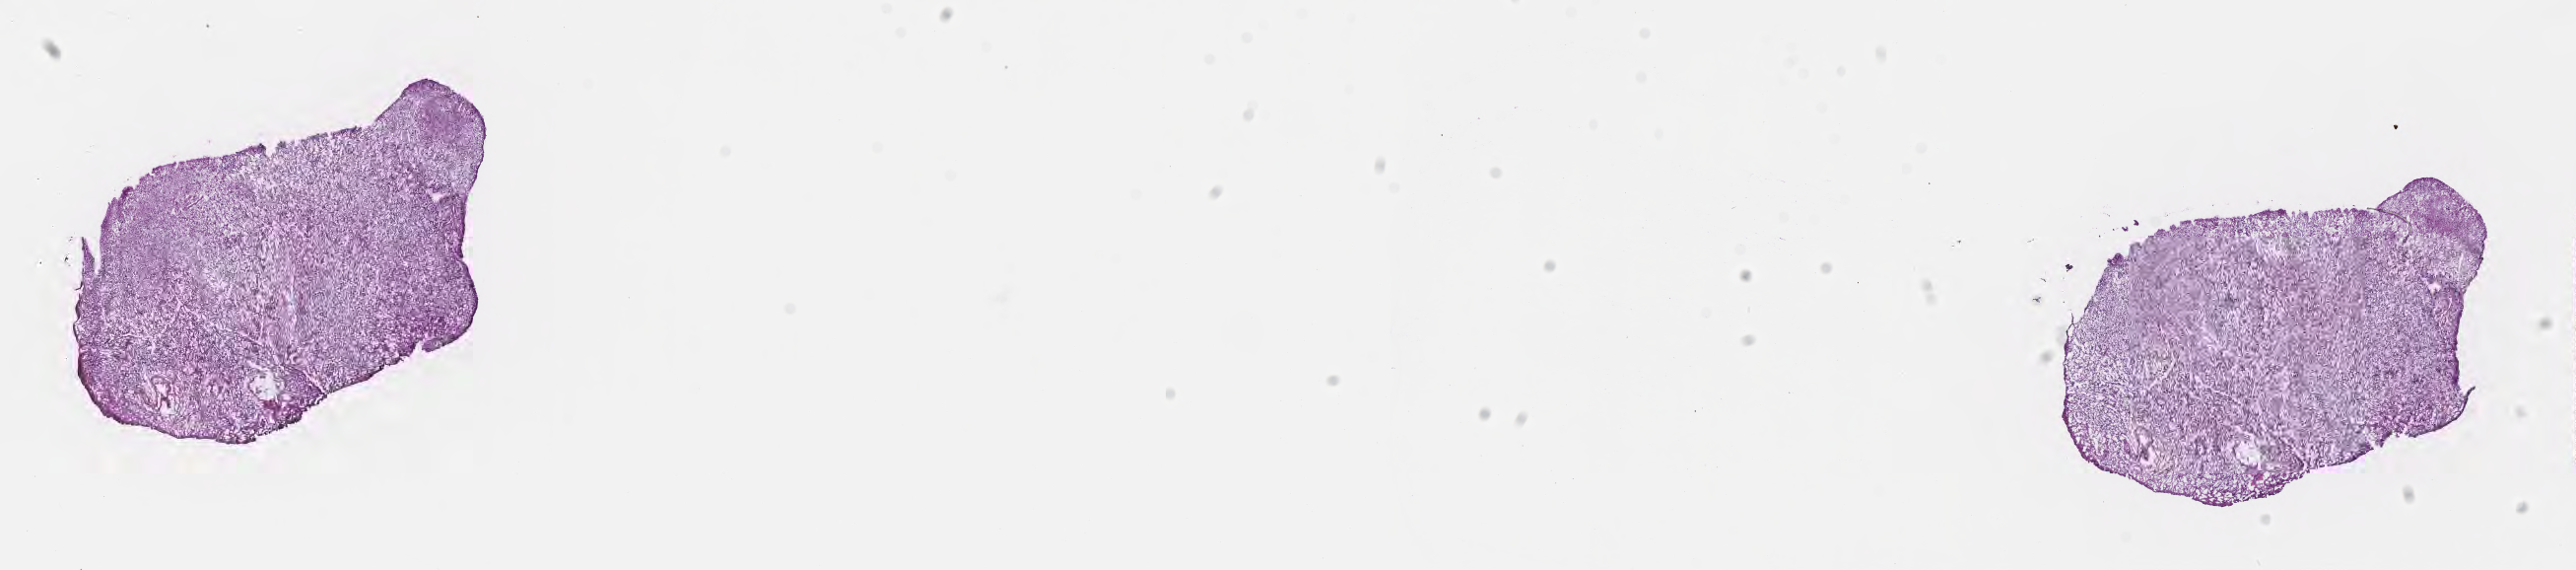
Whole-slide image, hematoxylin and eosin (H&E) stain — shown as a low-resolution overview of the whole scanned area (about 21.1 x 4.7 mm); cryosection; recurrent tumor; site: brain. Patient: male, age at initial diagnosis 49 years. Composition of this section per pathologist review: tumor cells 78%, tumor nuclei 90%, stromal cells 13%, necrosis 1%, normal cells 8%. Infiltration values recorded for this section: lymphocyte infiltration 0%, monocyte infiltration 0%, neutrophil infiltration 0%.
Patient diagnosis: Glioblastoma, NOS. Section: bottom of the tissue portion.